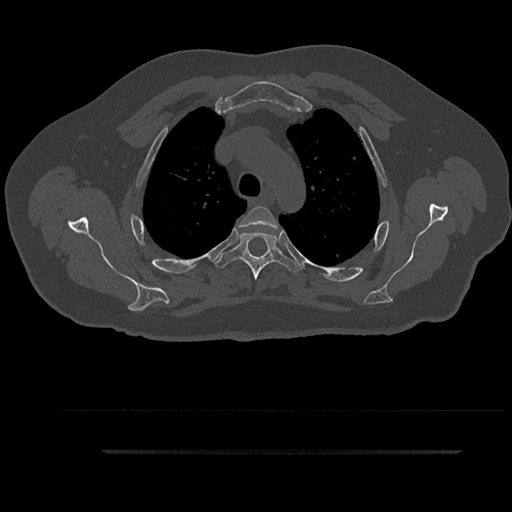
CT including the spine, one axial slice; position 685 of 797 along the scan axis; reconstruction kernel Br40s/3; bone window (W 1800 / L 400 HU); 512 × 512 image matrix, field of view 432 × 432 mm. Male patient, age 63 years. Case-level facts recorded for this patient, not image findings: primary cancer: renal.
Annotated regions visible in this slice (semi-automatically segmented with operator editing):
- T3 vertebra: bounding box [x1, y1, x2, y2] px = [240, 206, 279, 234]
- T4 vertebra: [214, 232, 300, 281]